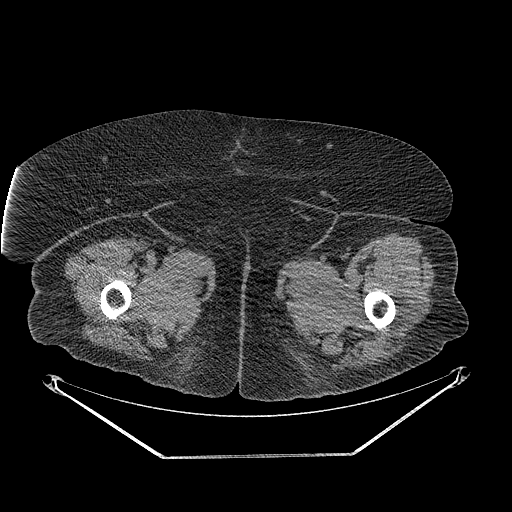
CT of an extremity soft-tissue mass (from a PET/CT study), one axial slice. Slice 262 of 267 in the series (ordered by position). 140 kVp. Soft-tissue window (W 400 / L 40 HU). 3.75 mm slice thickness. 512 × 512 image matrix, field of view 500 × 500 mm. Female patient. Case-level facts recorded for this patient, not image findings: histological type: undifferentiated – high grade; grade: high; site of the primary tumour: left thigh.
Structures marked on this image (expert contour drawn on MRI and transferred to this co-registered scan by the dataset authors):
- gross tumour volume including surrounding oedema: bounding box <402,304,407,309> (left, top, right, bottom; pixels)